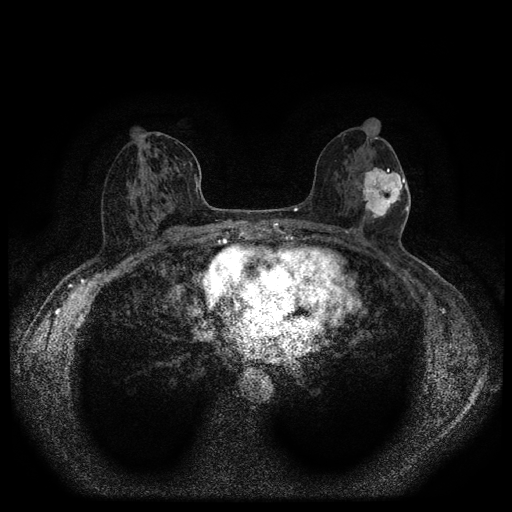
Breast MRI (dynamic contrast-enhanced, multi-phase), one axial slice. Position 53 of 116 along the scan axis. Dynamic contrast-enhanced series, time point 2 of 5 at this slice position (early post-contrast). 1.5 T. TE 2.7 ms, TR 5.4 ms. 2 mm slice thickness. 512 × 512 image matrix, field of view 330 × 330 mm. Female patient, age 56 years.
Outlined on this slice (semi-automatically segmented with operator editing):
- breast lesion (labelled 'tumour' in the annotation; benign lesions carry a separate 'benign' label): bounding box [x1, y1, x2, y2] px = [360, 165, 404, 222]